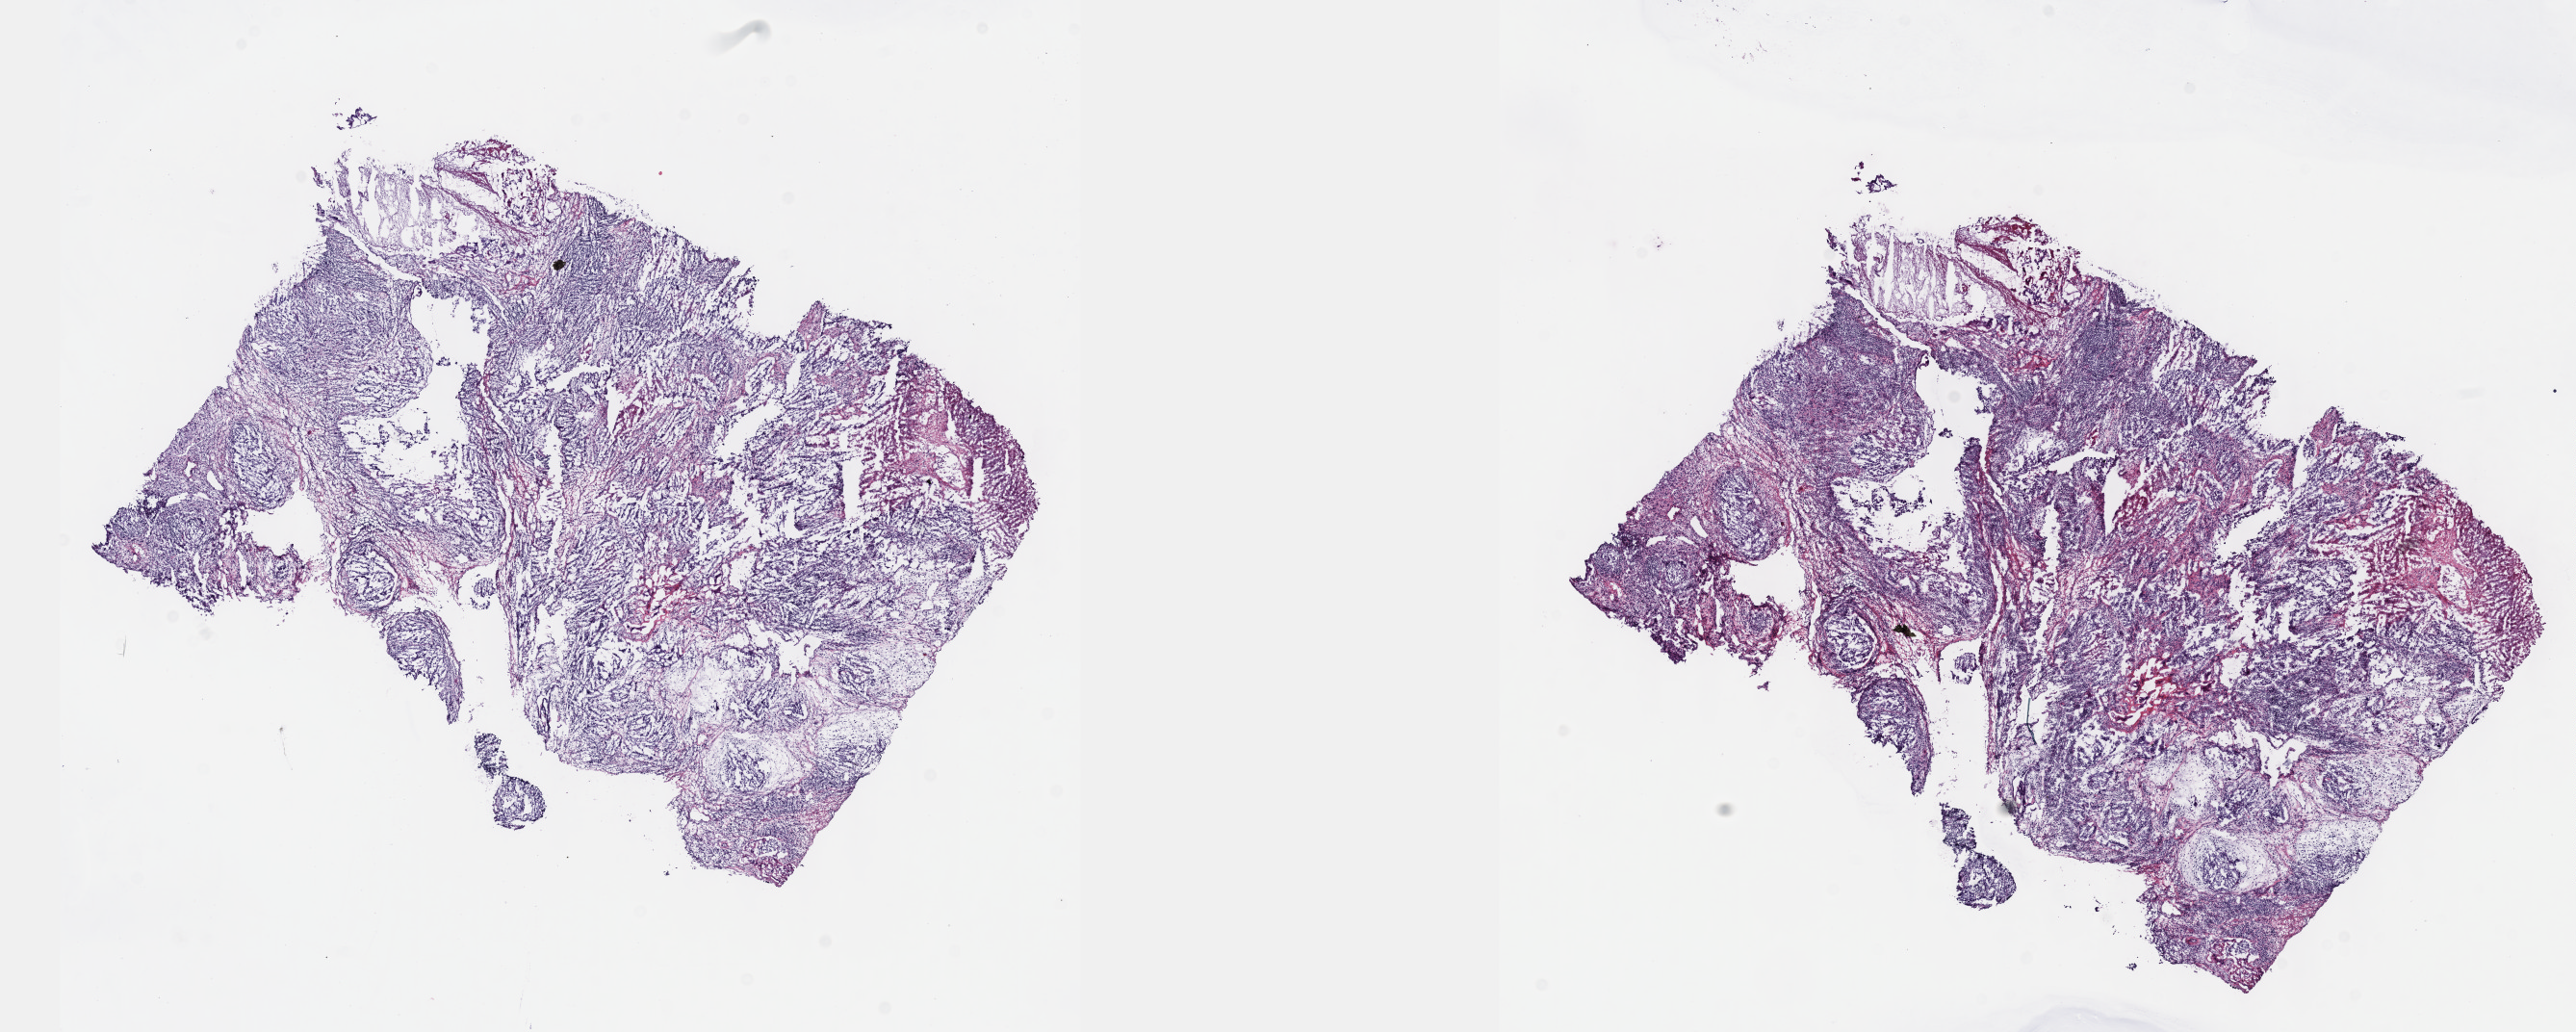
H&E-stained whole-slide image, shown as a low-resolution overview of the whole scanned area (about 21.6 x 8.7 mm). Male patient. Pathologist review of this section (percent, as recorded): tumour cells 80%, tumour nuclei 80%, normal cells 0%, stromal cells 20%, necrosis 0%. Inflammatory infiltration, as recorded: lymphocyte infiltration 40%, monocyte infiltration 20%, neutrophil infiltration 20%.
Specimen: frozen section from the top of the tissue portion; primary tumour sample from the testis.